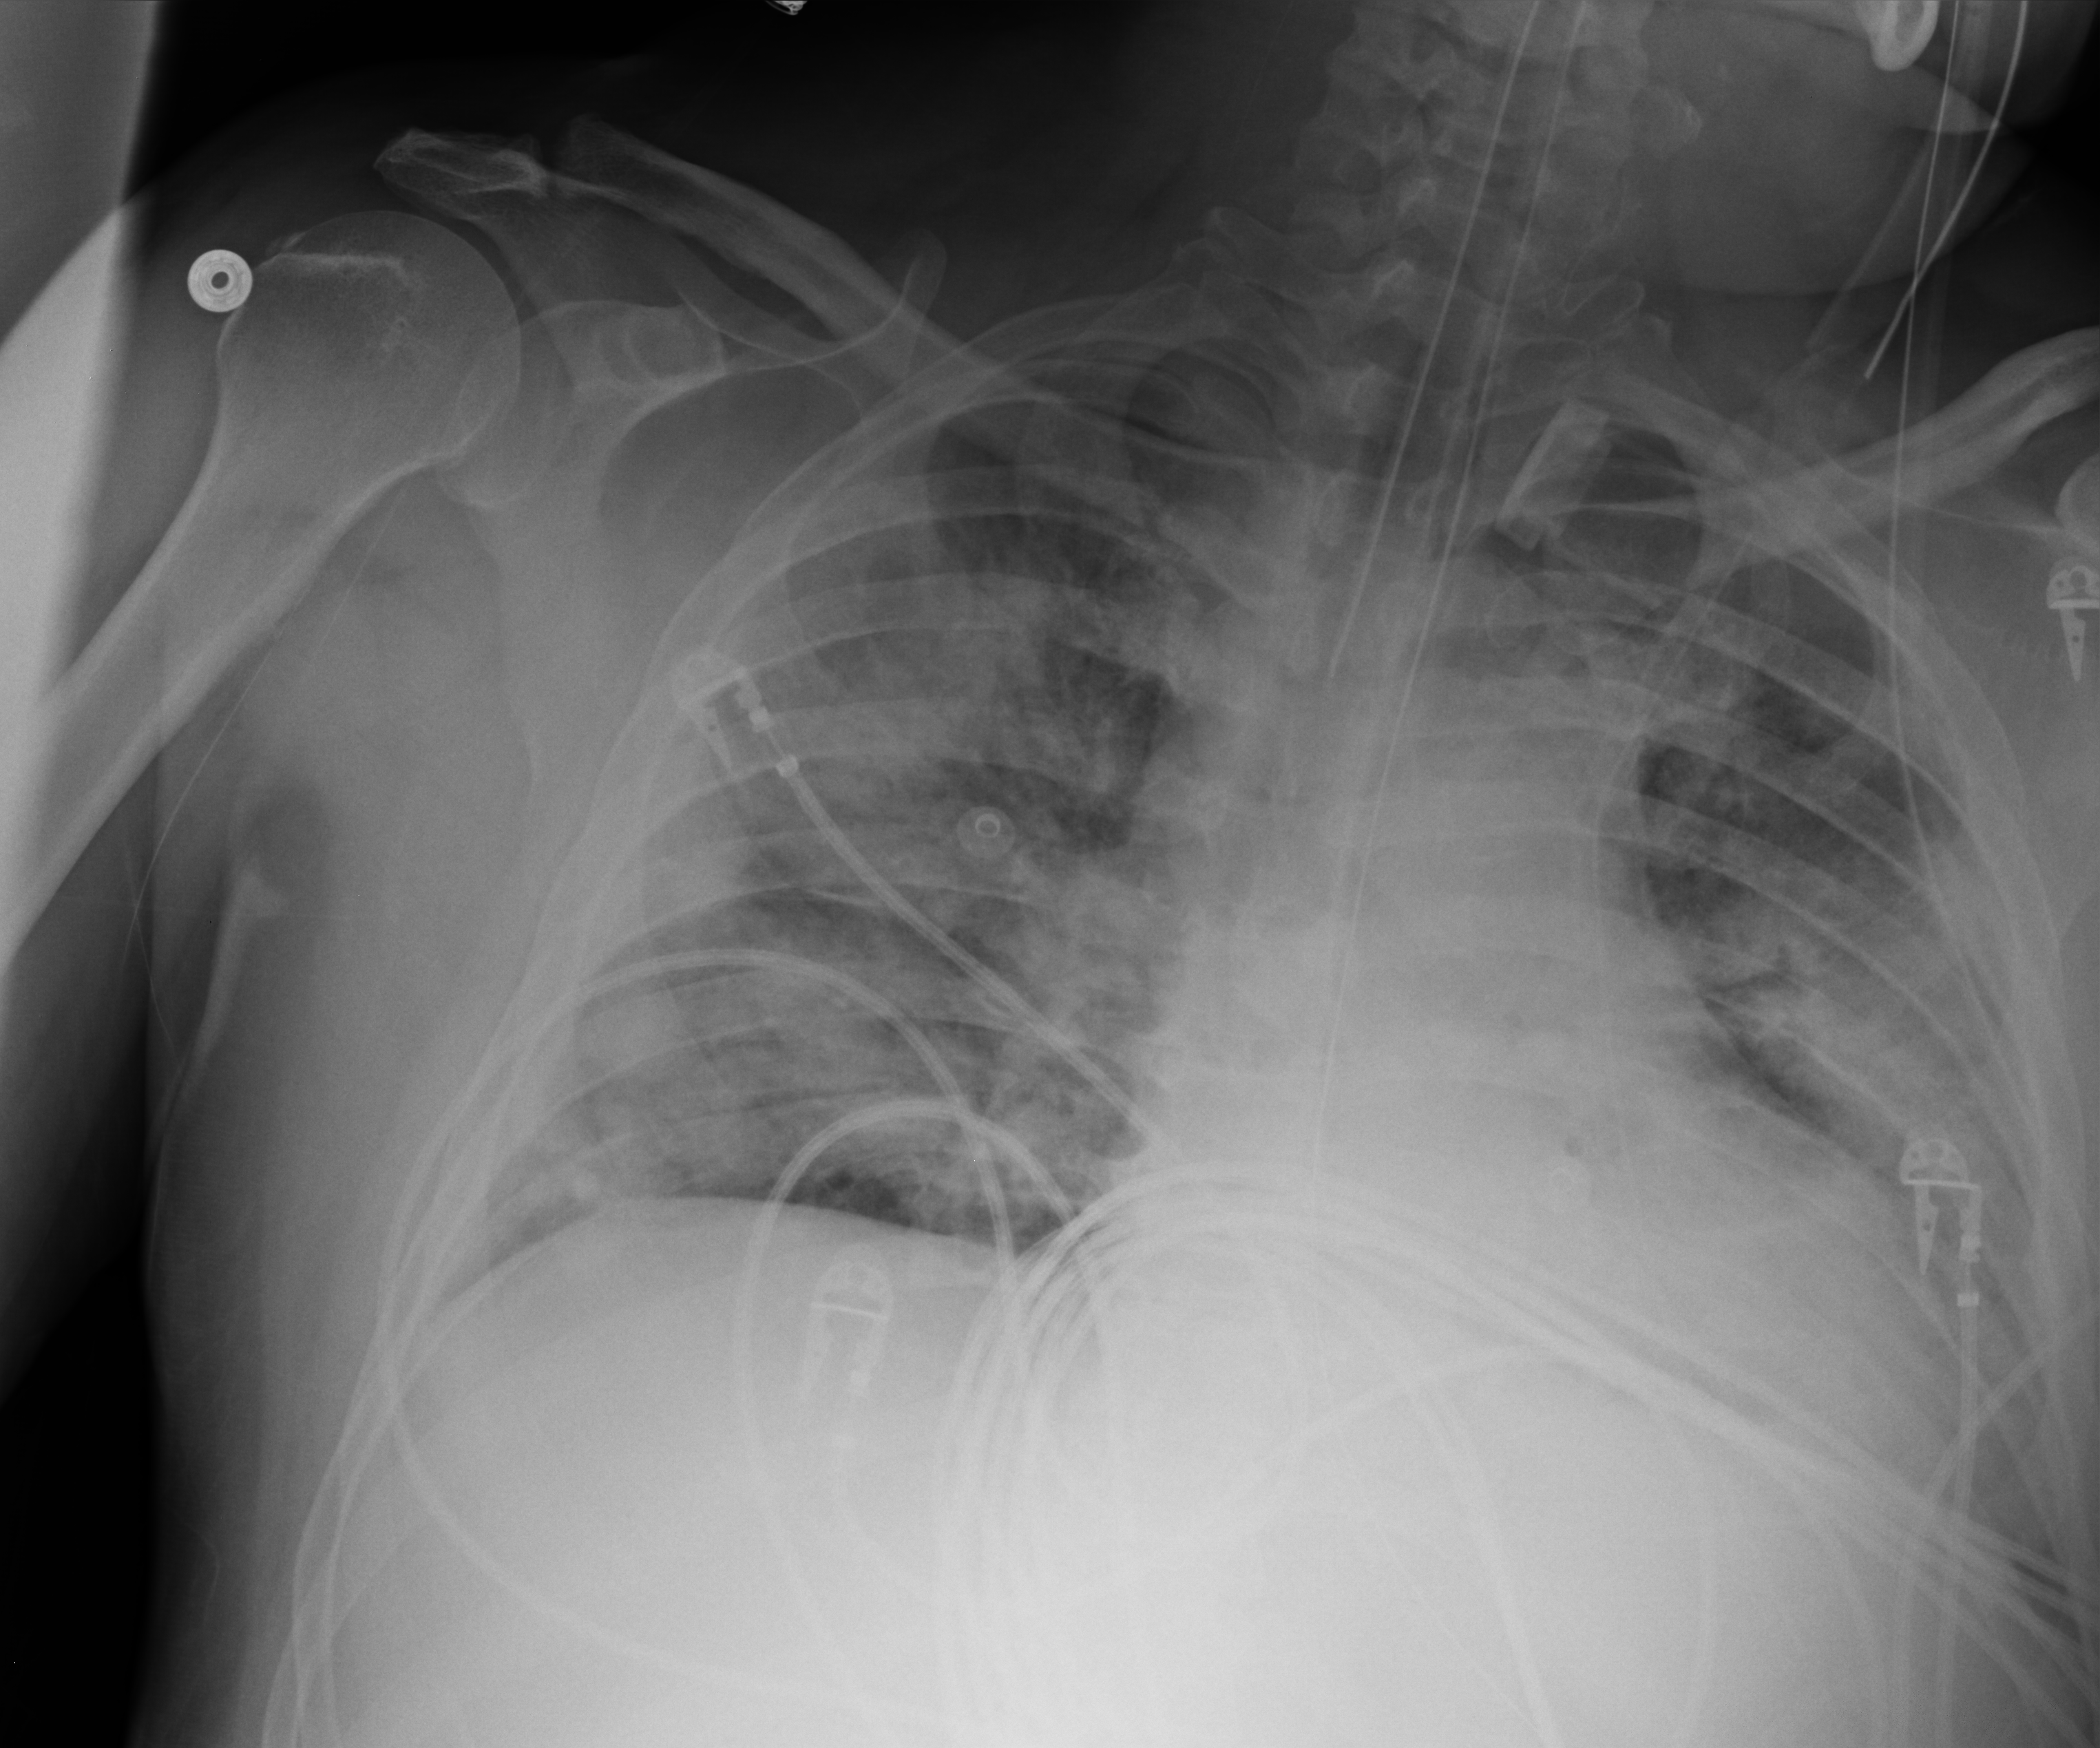
Portable chest radiograph, anteroposterior (AP) projection. Patient hospitalised with COVID-19; male, aged 18–59 years.
Admission-level facts for this patient (not findings on this image; timing relative to this image not recorded): mechanically ventilated during this hospital stay: yes.